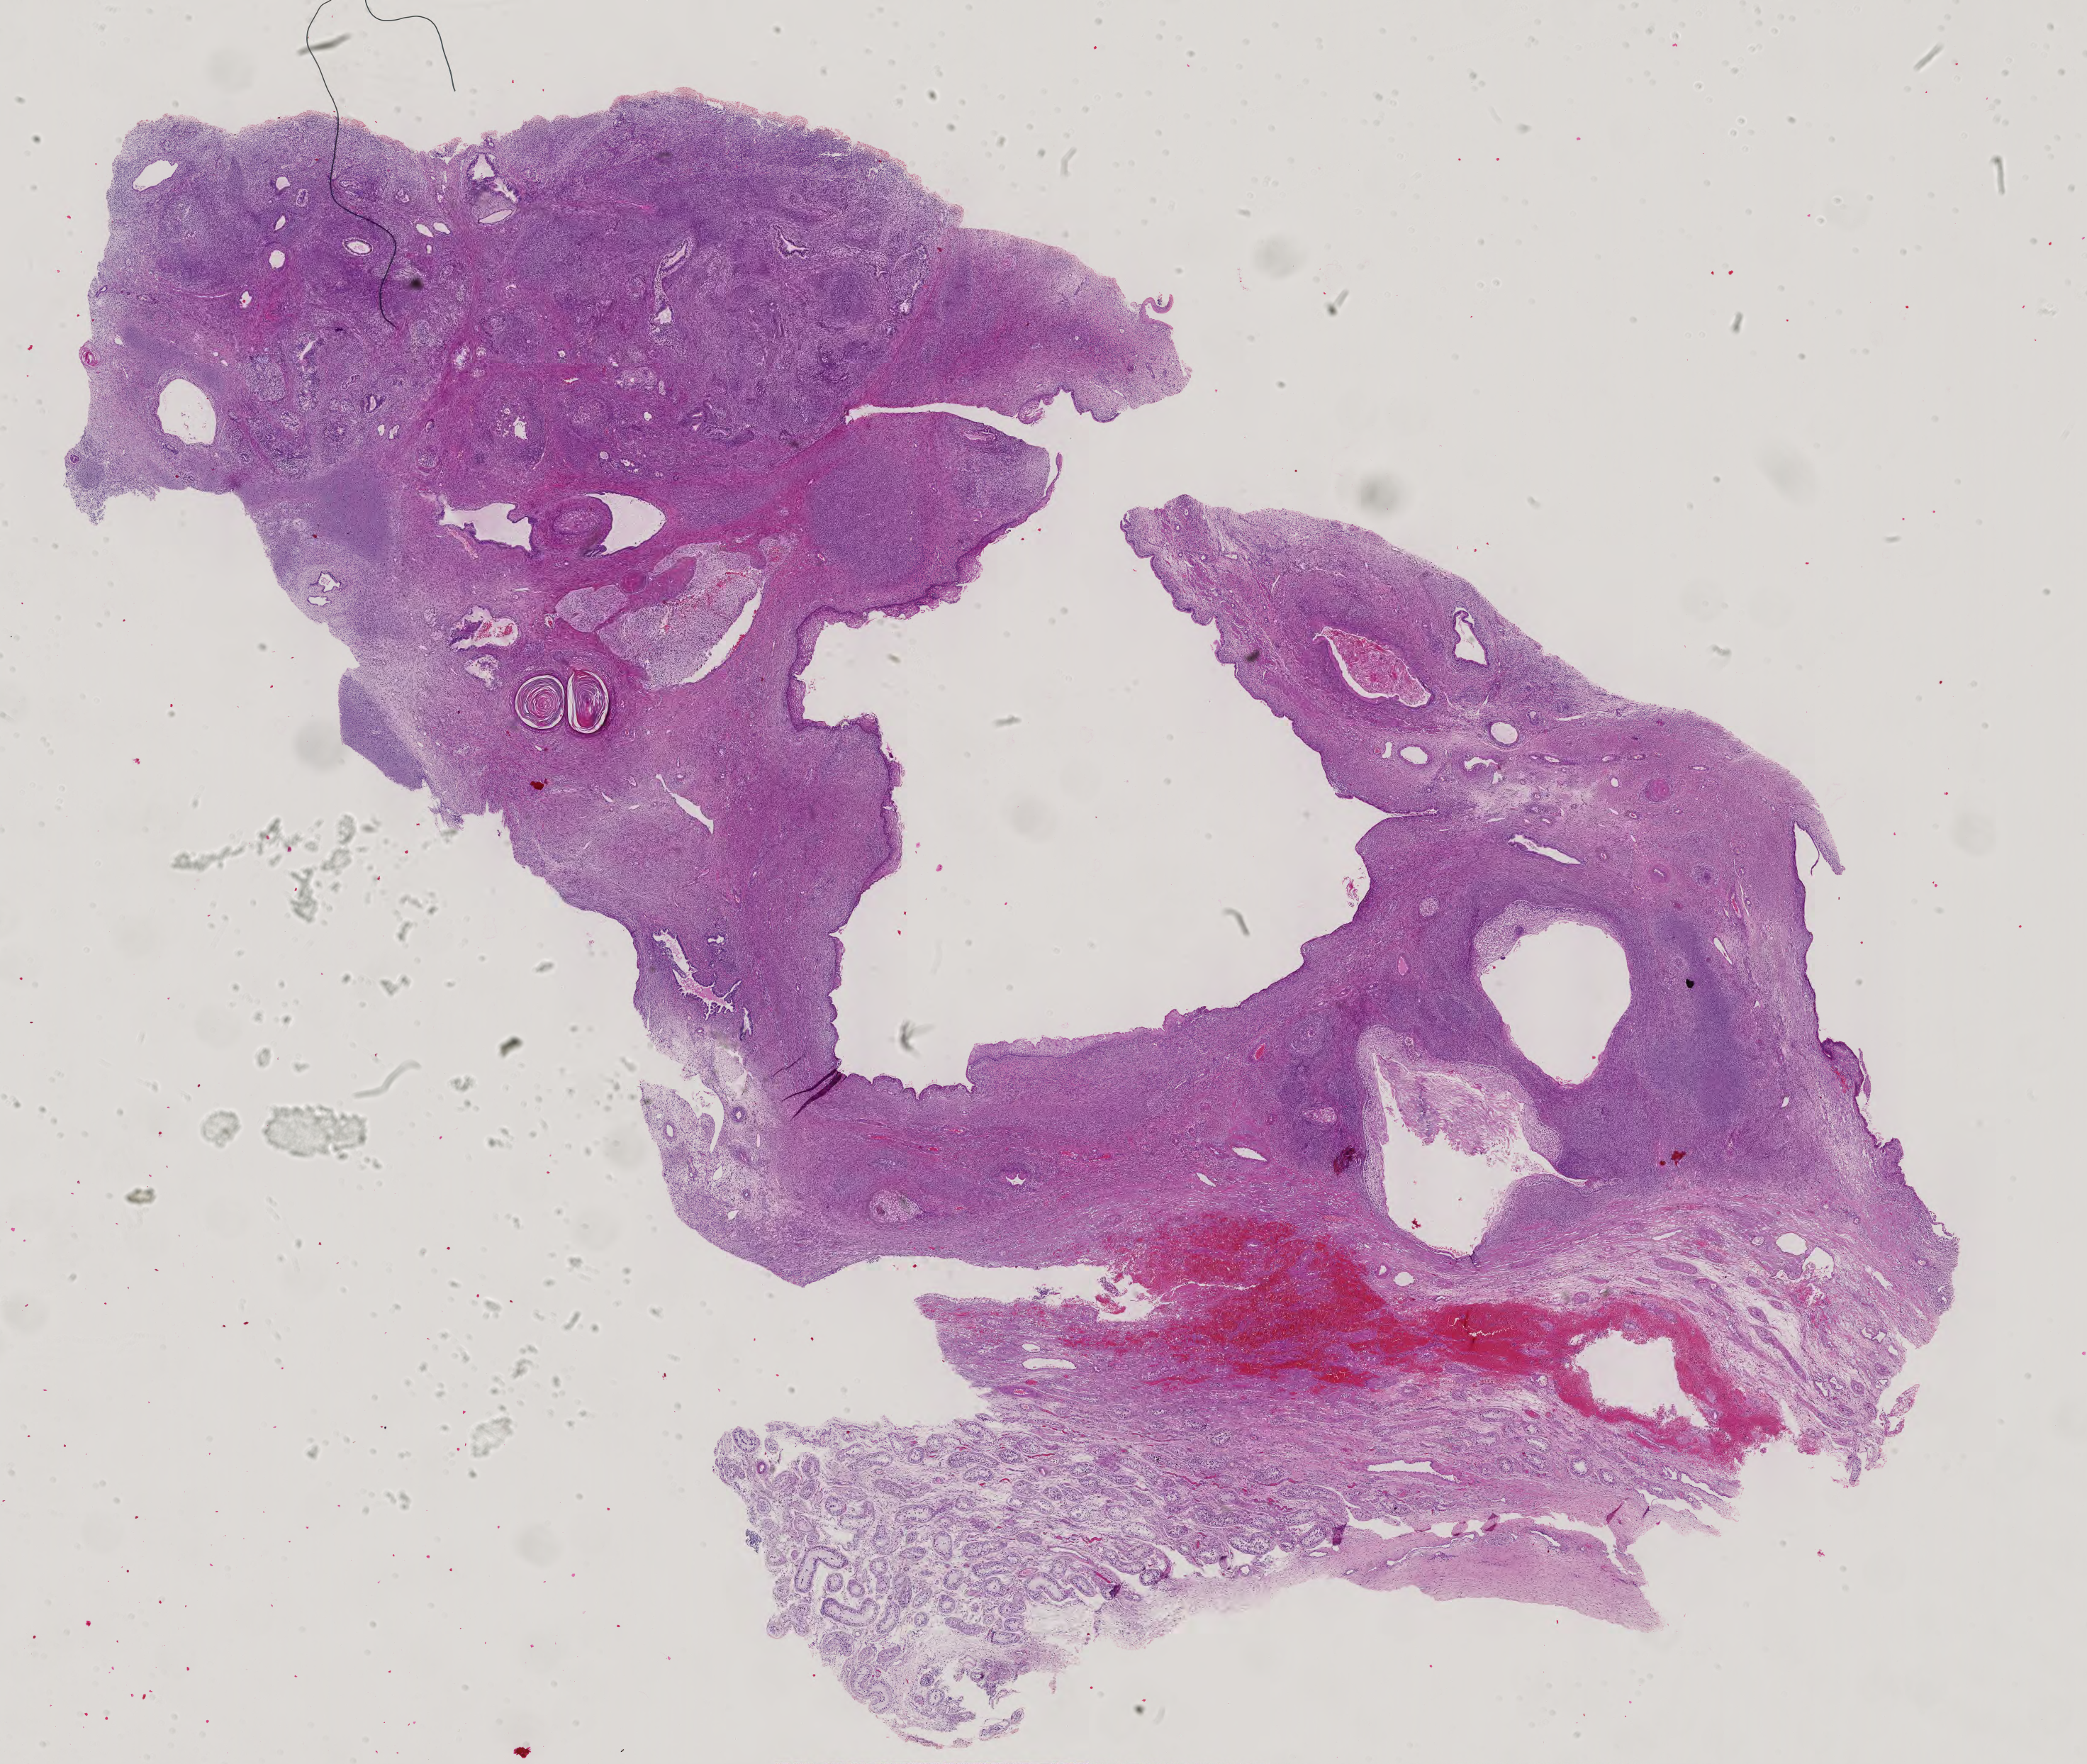
Whole-slide histology image, Hematoxylin and eosin (H&E) stained — shown as a low-resolution overview of the whole scanned area (about 21.5 x 18.1 mm). Male patient.
Specimen: FFPE section; testis, primary tumour sample.